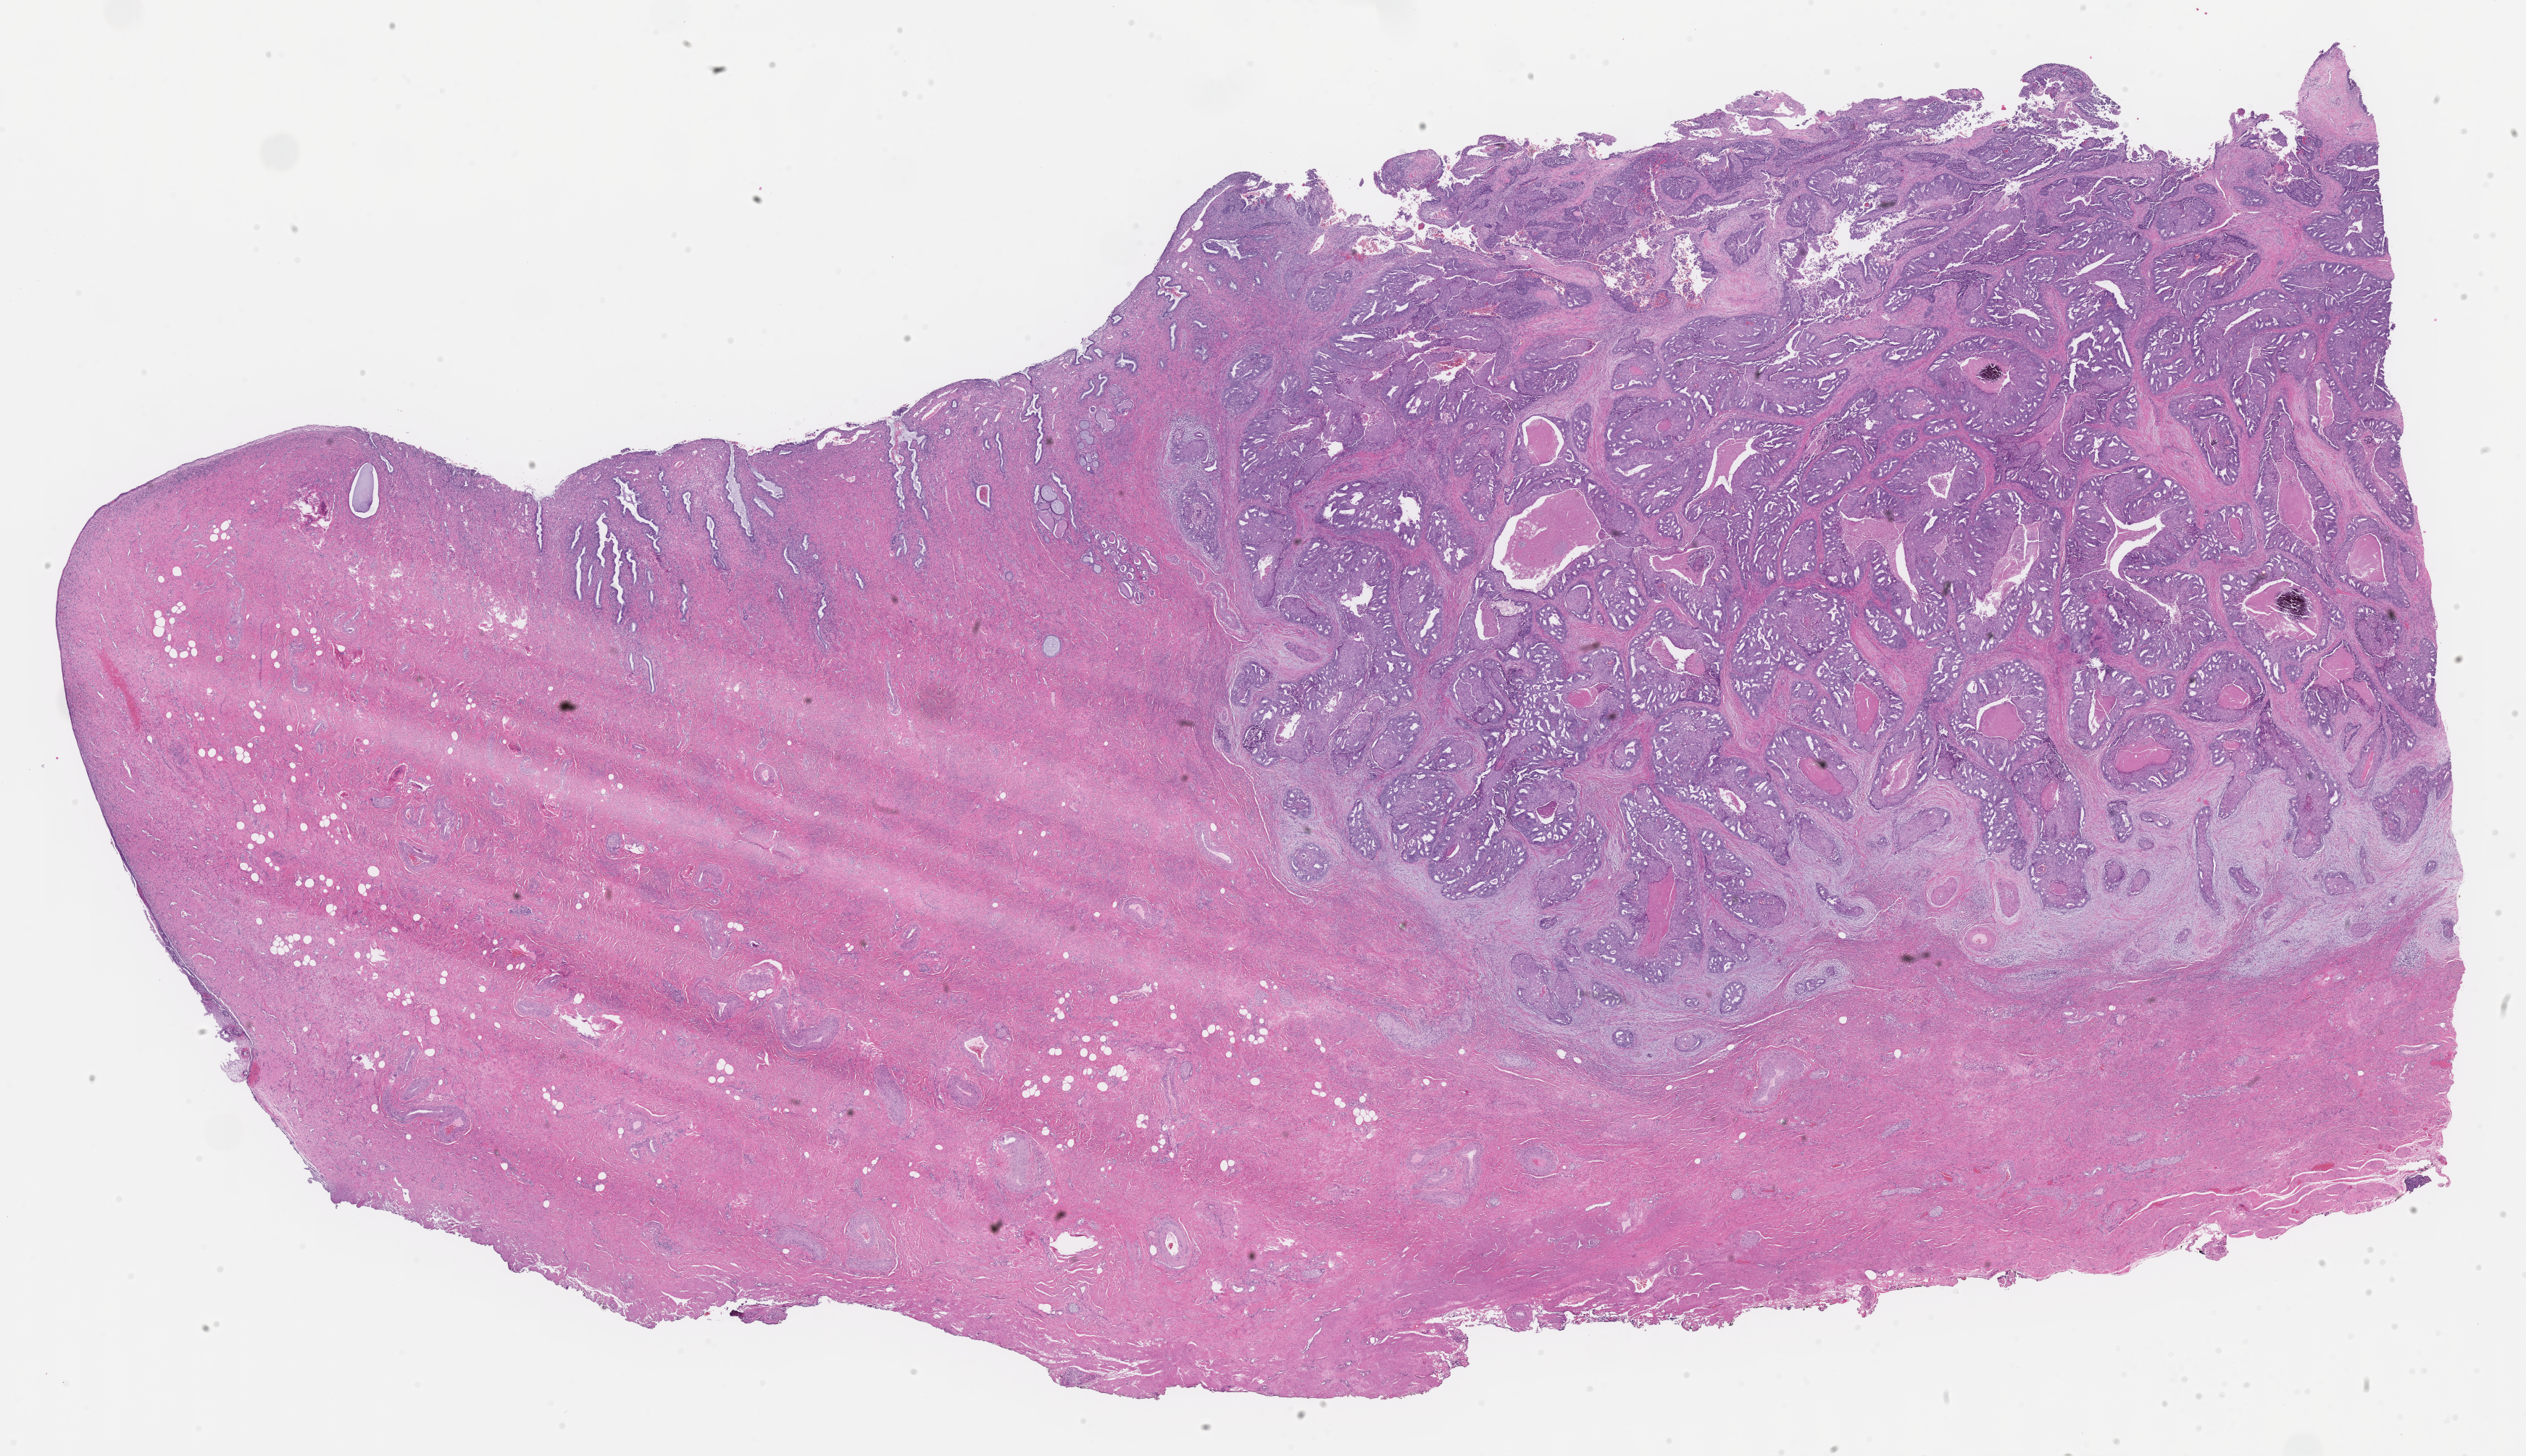
Whole-slide image, hematoxylin and eosin (H&E) stain — whole scanned area (about 28.1 x 16.2 mm) shown as a low-resolution overview; formalin-fixed paraffin-embedded section; specimen: primary tumor; site: endometrium. Female, age 53 years at initial diagnosis. Tumor grade: G2 (moderately differentiated). Composition of this section per pathologist review: tumor cells 22%, tumor nuclei 90%, stromal cells 74%, necrosis 2%, normal cells 2%. Inflammatory infiltration, as recorded: lymphocyte infiltration 4%, monocyte infiltration 0%, neutrophil infiltration 0%.
AJCC pathologic stage: Stage II. Diagnosis: Endometrioid adenocarcinoma, NOS. Section: bottom of the tissue portion.